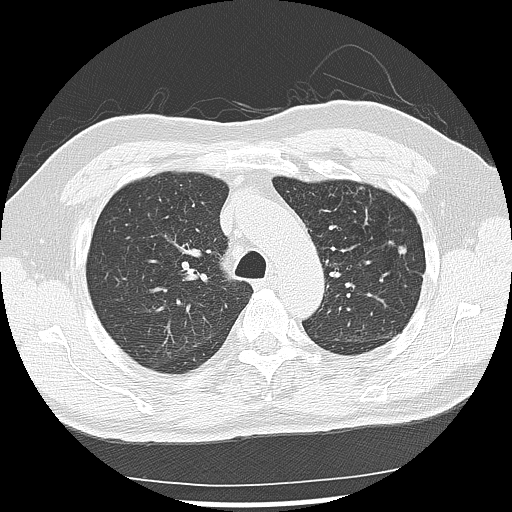
Low-dose screening chest CT, one axial slice. Position 99 of 142 along the scan axis. 120 kVp. Lung window (W 1500 / L -600 HU). 2.5 mm slice thickness. 512 × 512 image matrix.
Outlined on this slice (expert manual segmentation):
- lesion 4 (nodule, upper lobe of left lung): bounding box <398,246,407,255> (left, top, right, bottom; pixels)